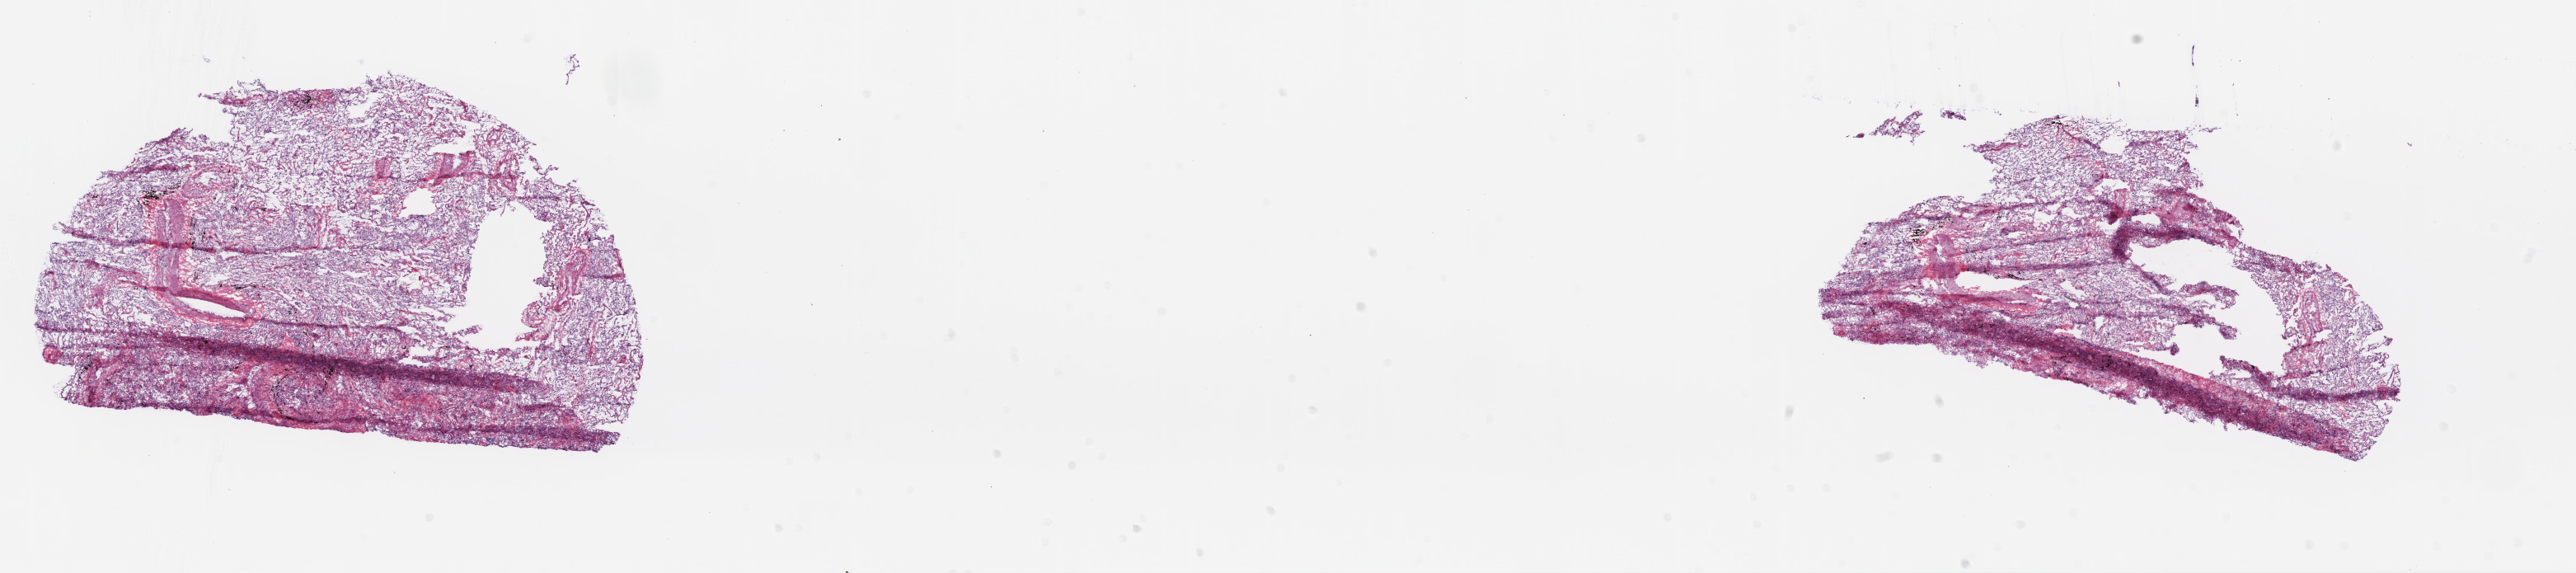
Hematoxylin and eosin (H&E) stained whole-slide image — low-resolution overview of the scanned area, about 25.1 x 5.6 mm (acquisition: 20x scan); frozen section; lung, solid tissue normal (non-tumour tissue) sample. Male, age 72 years at initial diagnosis.
This section: solid tissue normal (non-tumour) sample from the same patient. Patient diagnosis: Squamous cell carcinoma, NOS (upper lobe, lung).